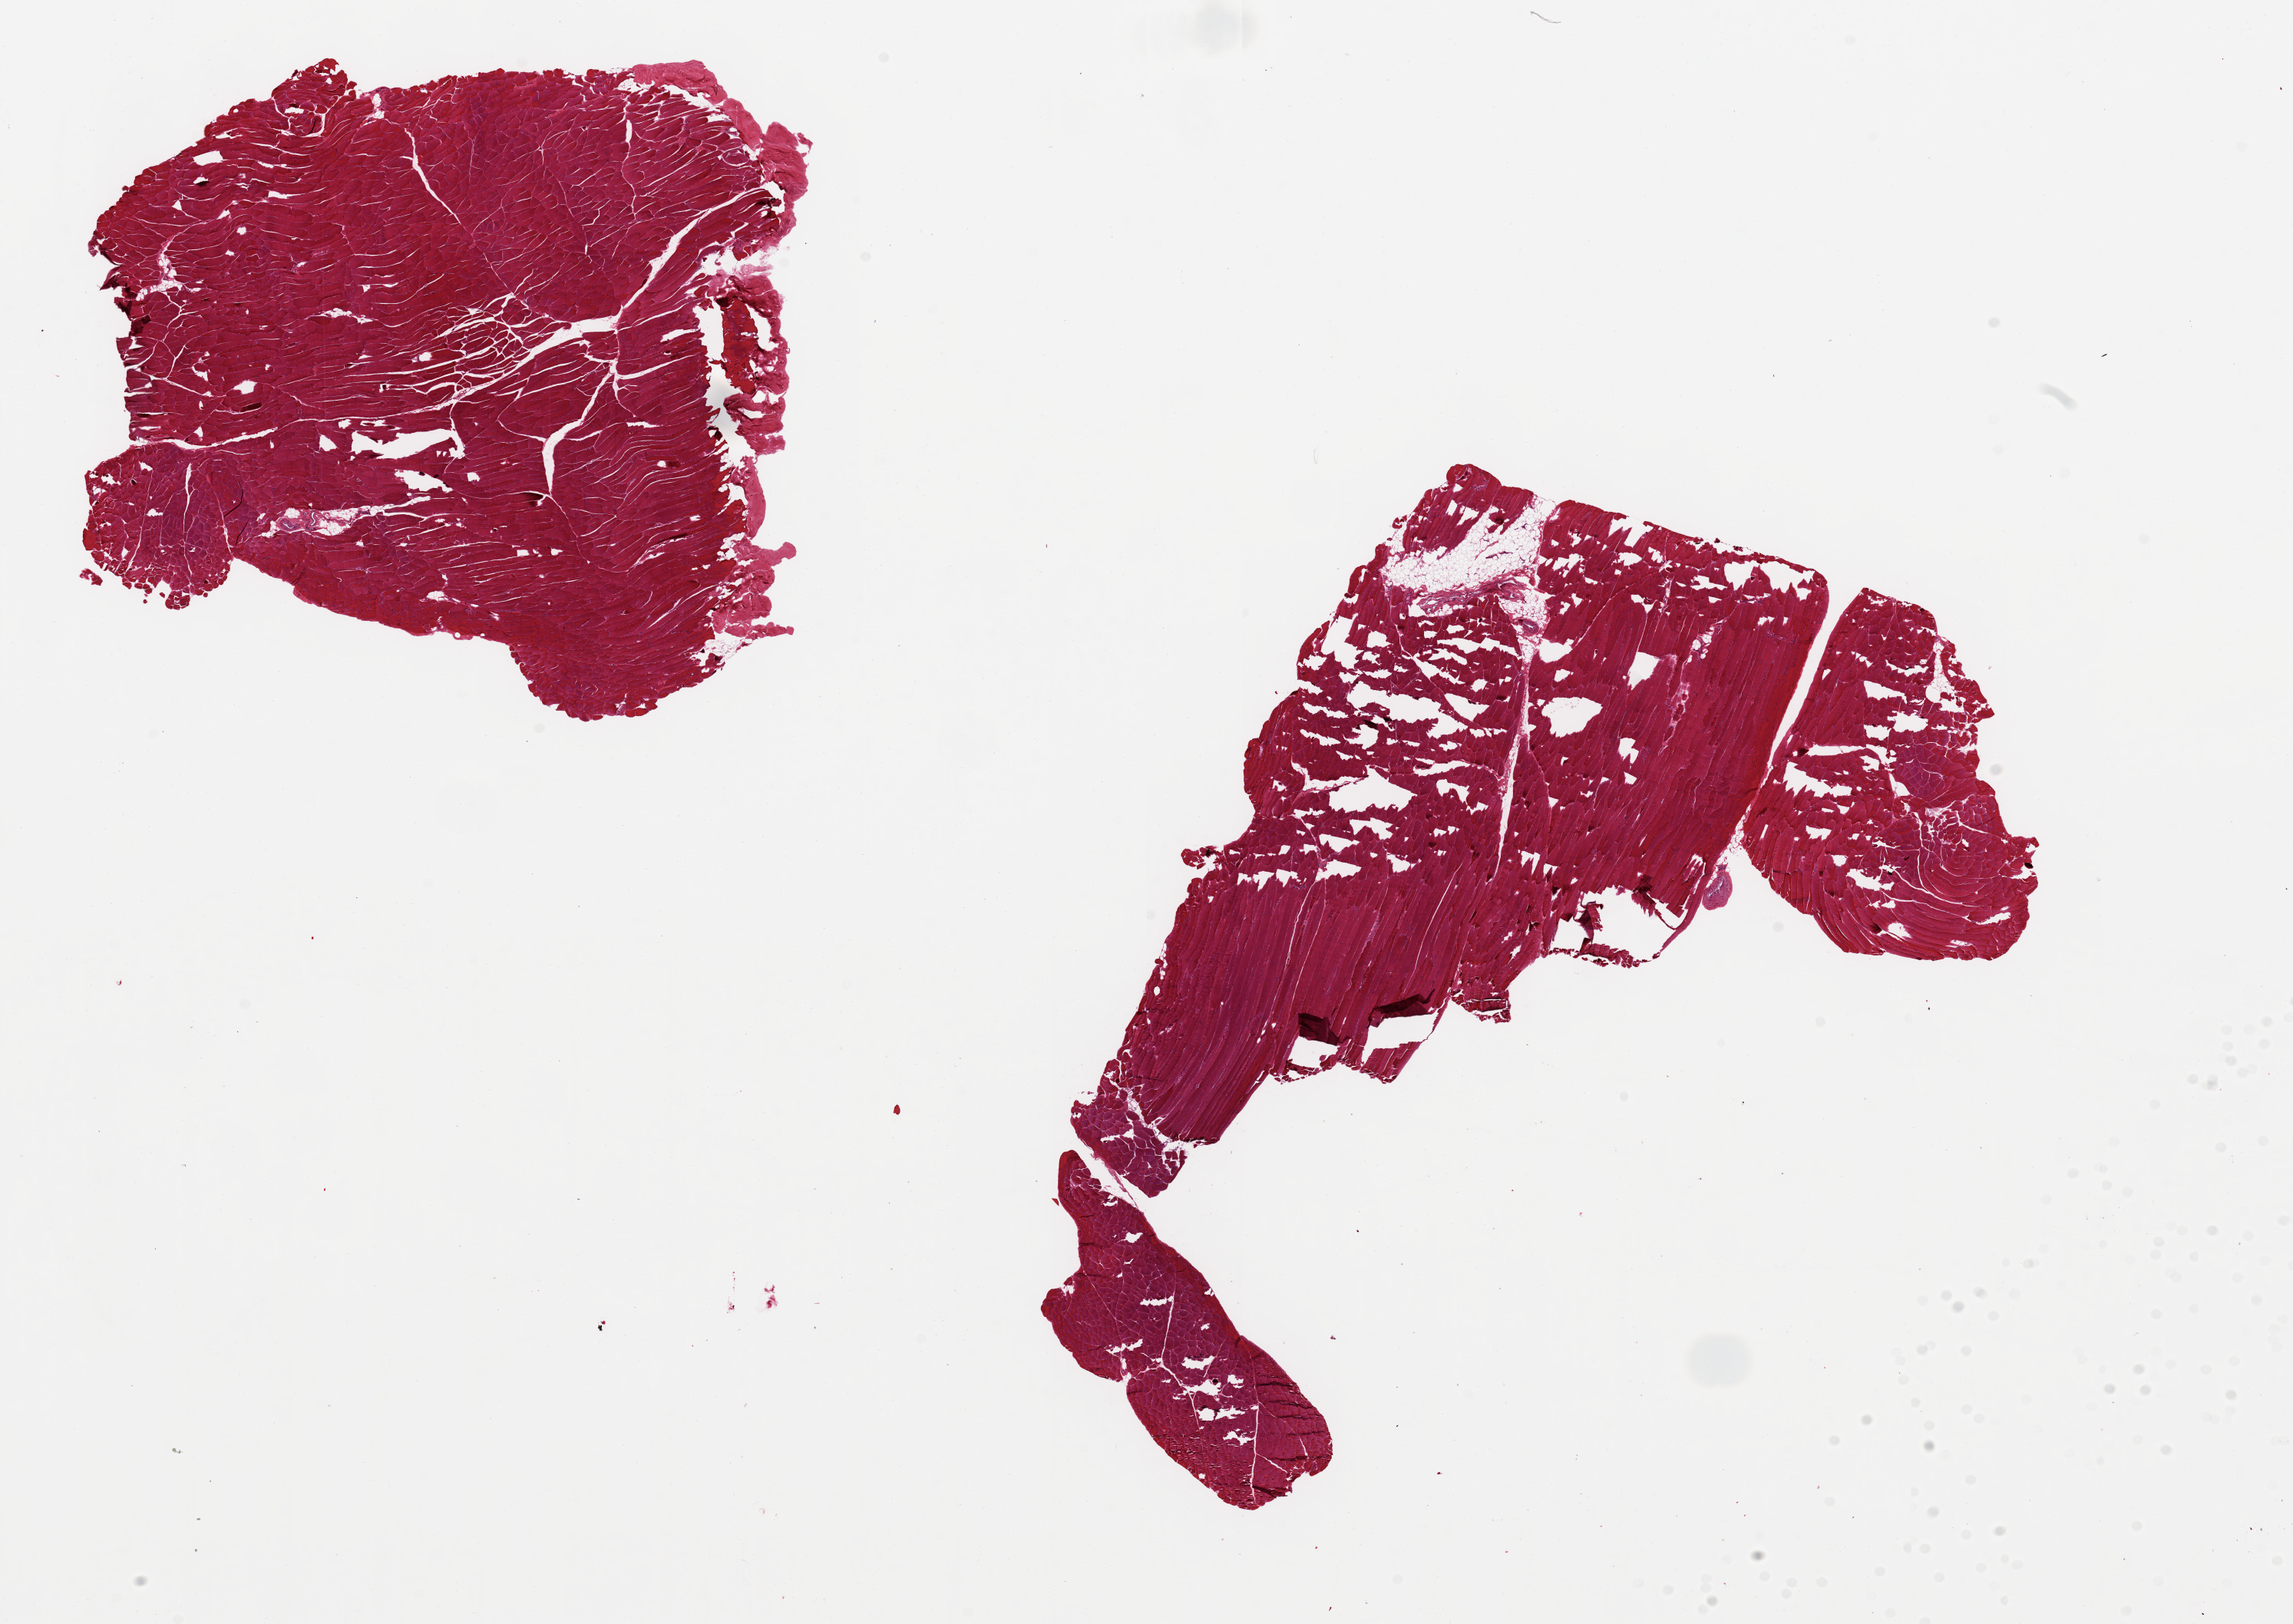
Digitized hematoxylin and eosin (H&E)-stained section — low-resolution overview of the scanned area, about 23.6 x 16.7 mm; PAXgene-fixed paraffin-embedded (PFPE) section; section of skeletal muscle (target tissue); donor tissue sample.
• review note (as recorded): 2 pieces ~9x8 & 6x7 mm pieces, large areas (>50%) with tears in the larger piece, probable poor fixation